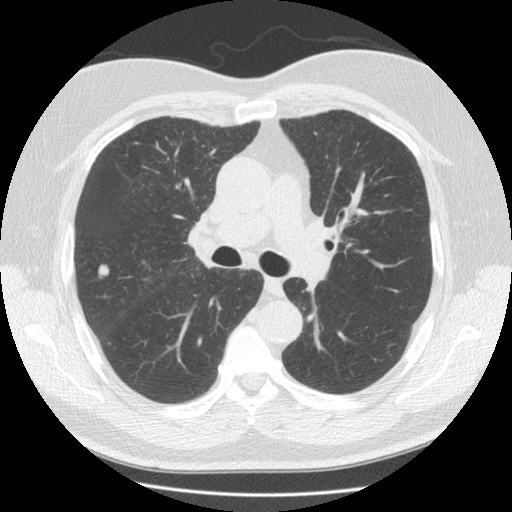
Chest CT (low-dose screening protocol), one axial image. Third screening round (two years after baseline). Lung window (W 1500 / L -600 HU). 2.5 mm slice thickness. Slice 59 of 146 in the series. 512 × 512 image matrix, field of view 350 × 350 mm. Male, age 65 years at enrolment. Former smoker at enrolment.
- Expert-annotated lung lesion, bounding box (x1, y1, x2, y2) in pixels: (90, 258, 117, 288).
- Screening reader's record for this exam (one nodule recorded; not confirmed to be the boxed lesion): non-calcified nodule or mass ≥4 mm, right upper lobe, 12 × 12 mm, smooth margins, soft tissue attenuation, pre-existing on the prior screen: yes; interval growth: yes.
- Official screen result: positive, other.
- Later outcome: lung cancer diagnosed 54 days after this screen — adenocarcinoma, NOS, right upper lobe, poorly differentiated (G3), stage IA (AJCC 6th edition), 17 mm at pathology.